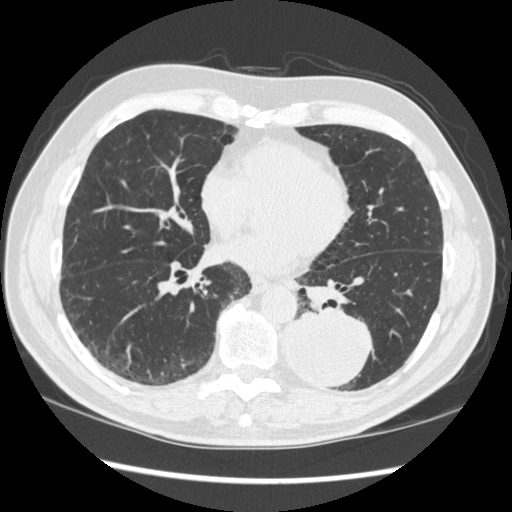
Low-dose screening chest CT, one axial slice; slice 137 of 348 in the series (ordered by position); lung window (W 1500 / L -600 HU); 1.25 mm slice thickness; 512 × 512 image matrix.
Outlined on this slice (manually delineated by an expert):
- lesion 1 (tumor, lower lobe of left lung): box from (x=283, y=309) to (x=373, y=387) px